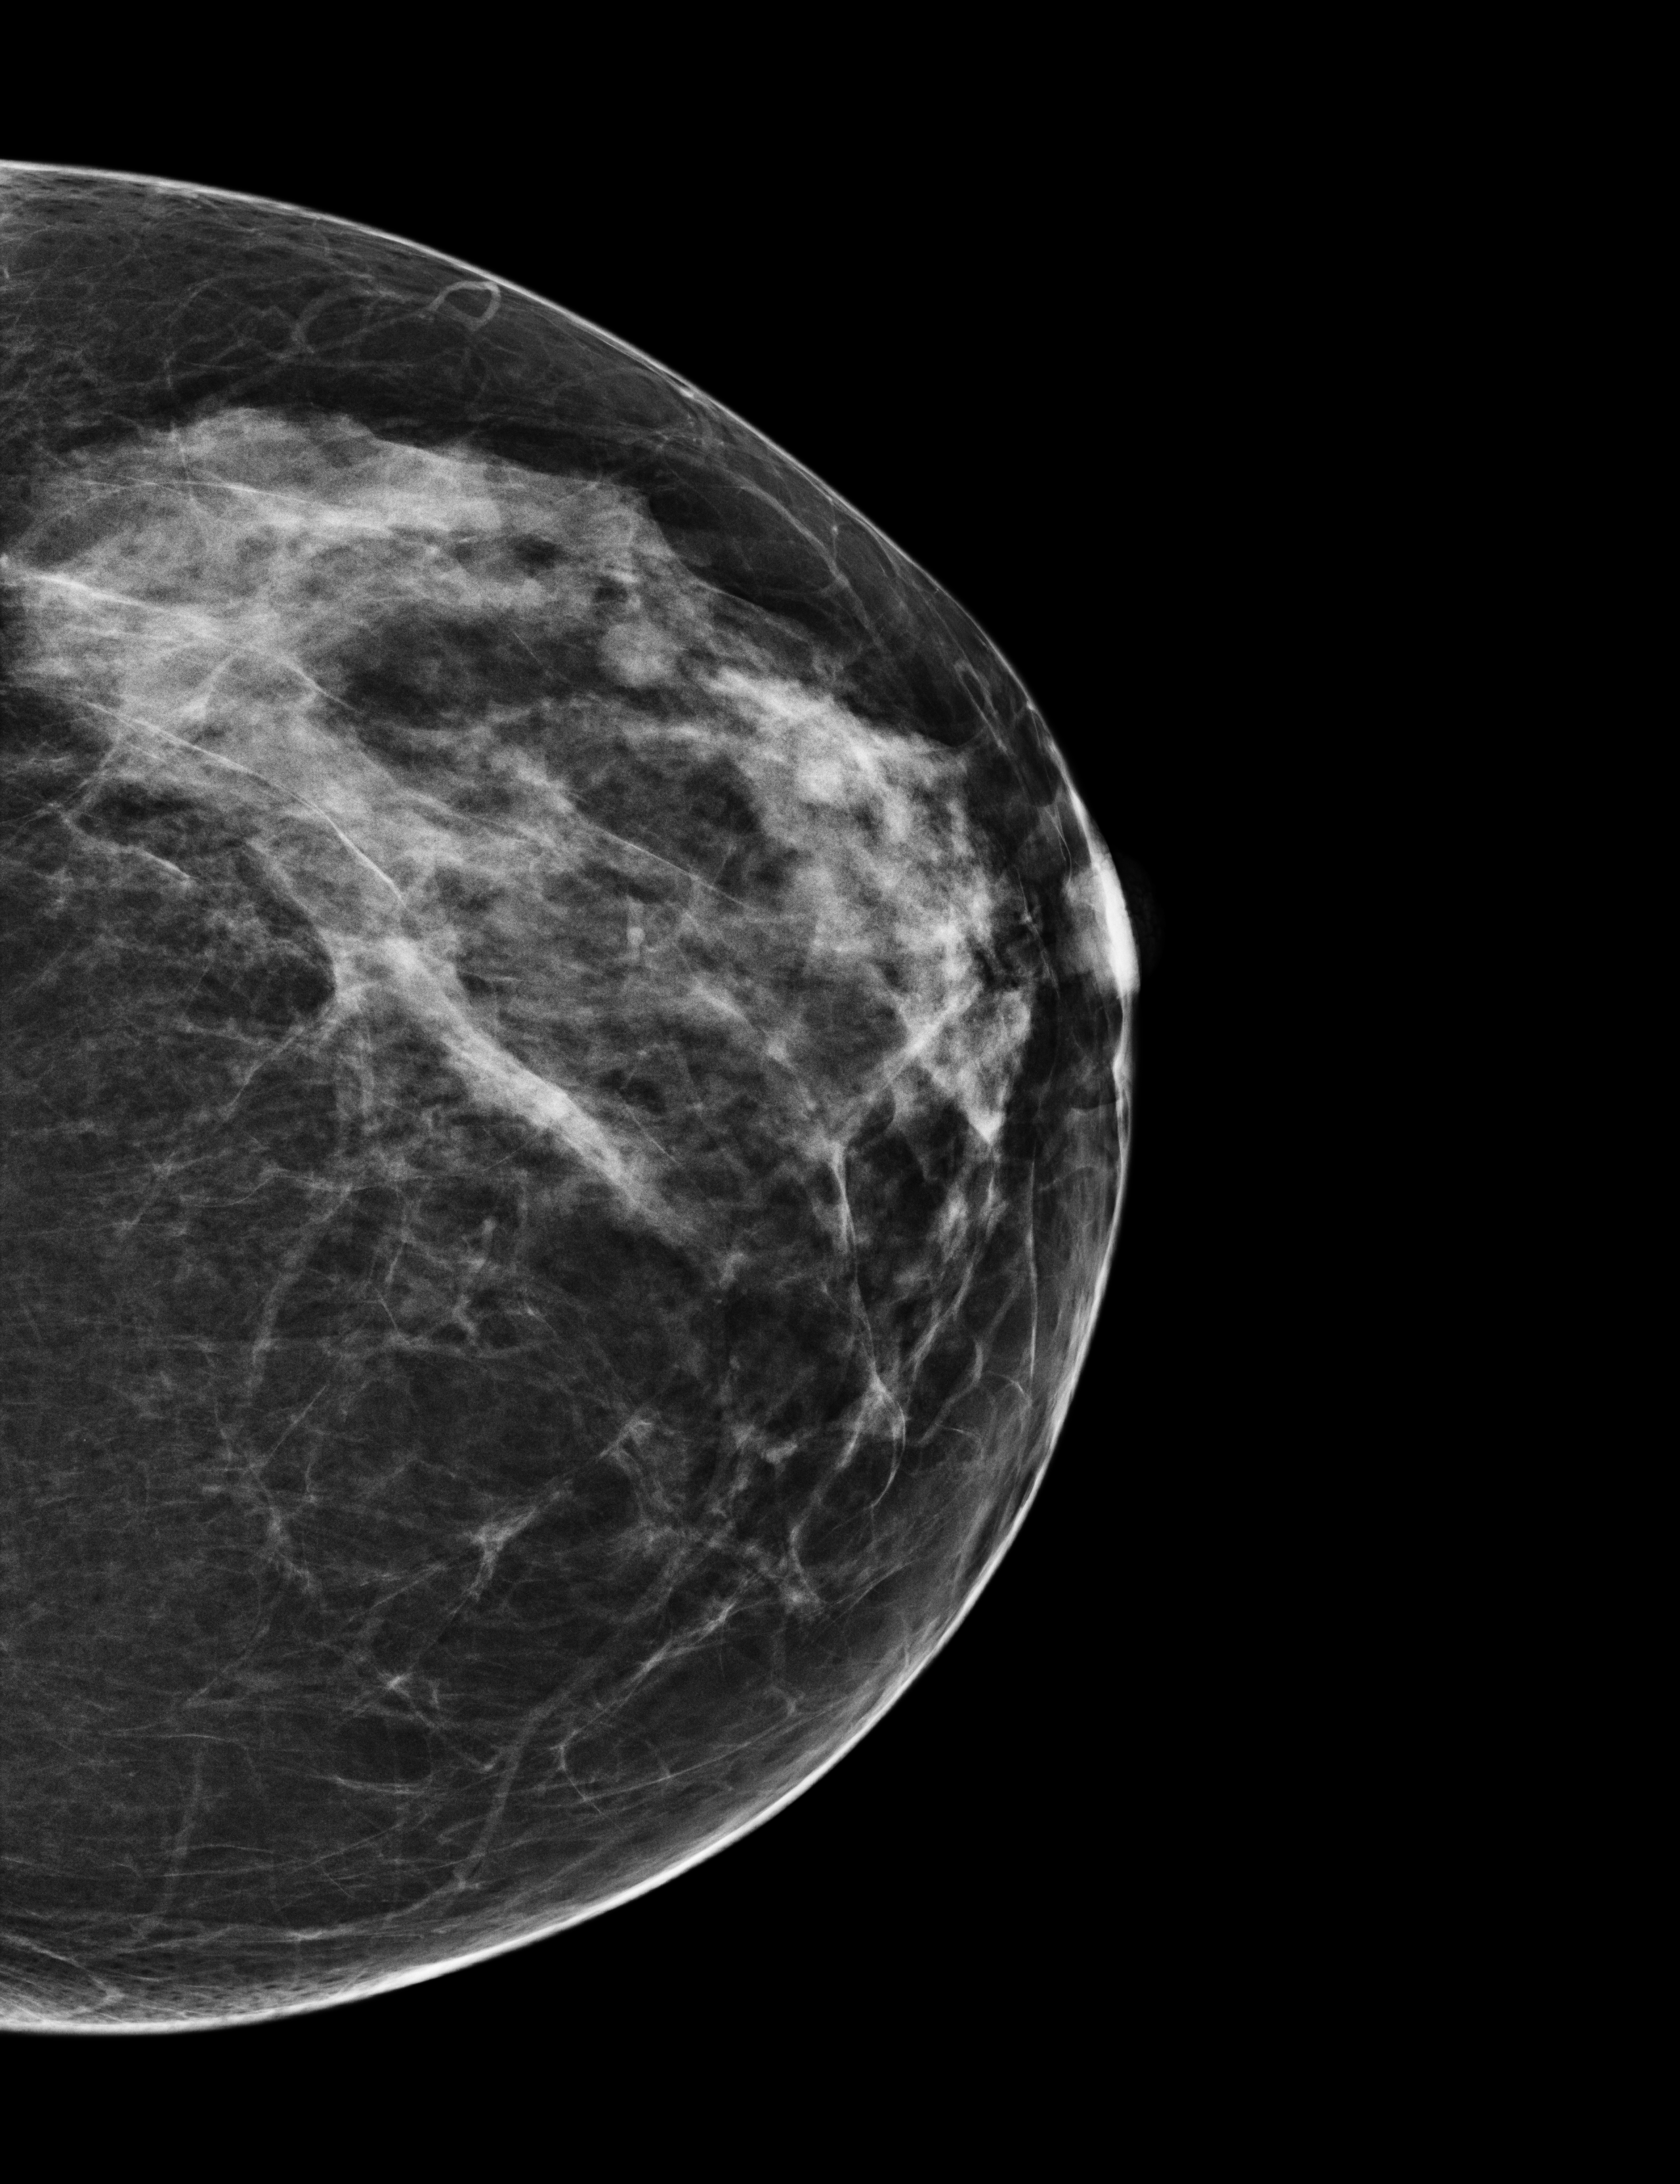
Annual screening mammography examination, system: Selenia Dimensions. Patient aged 42 years (female).
Image type: full-field digital mammogram. Breast: left. Projection: cranio-caudal projection.